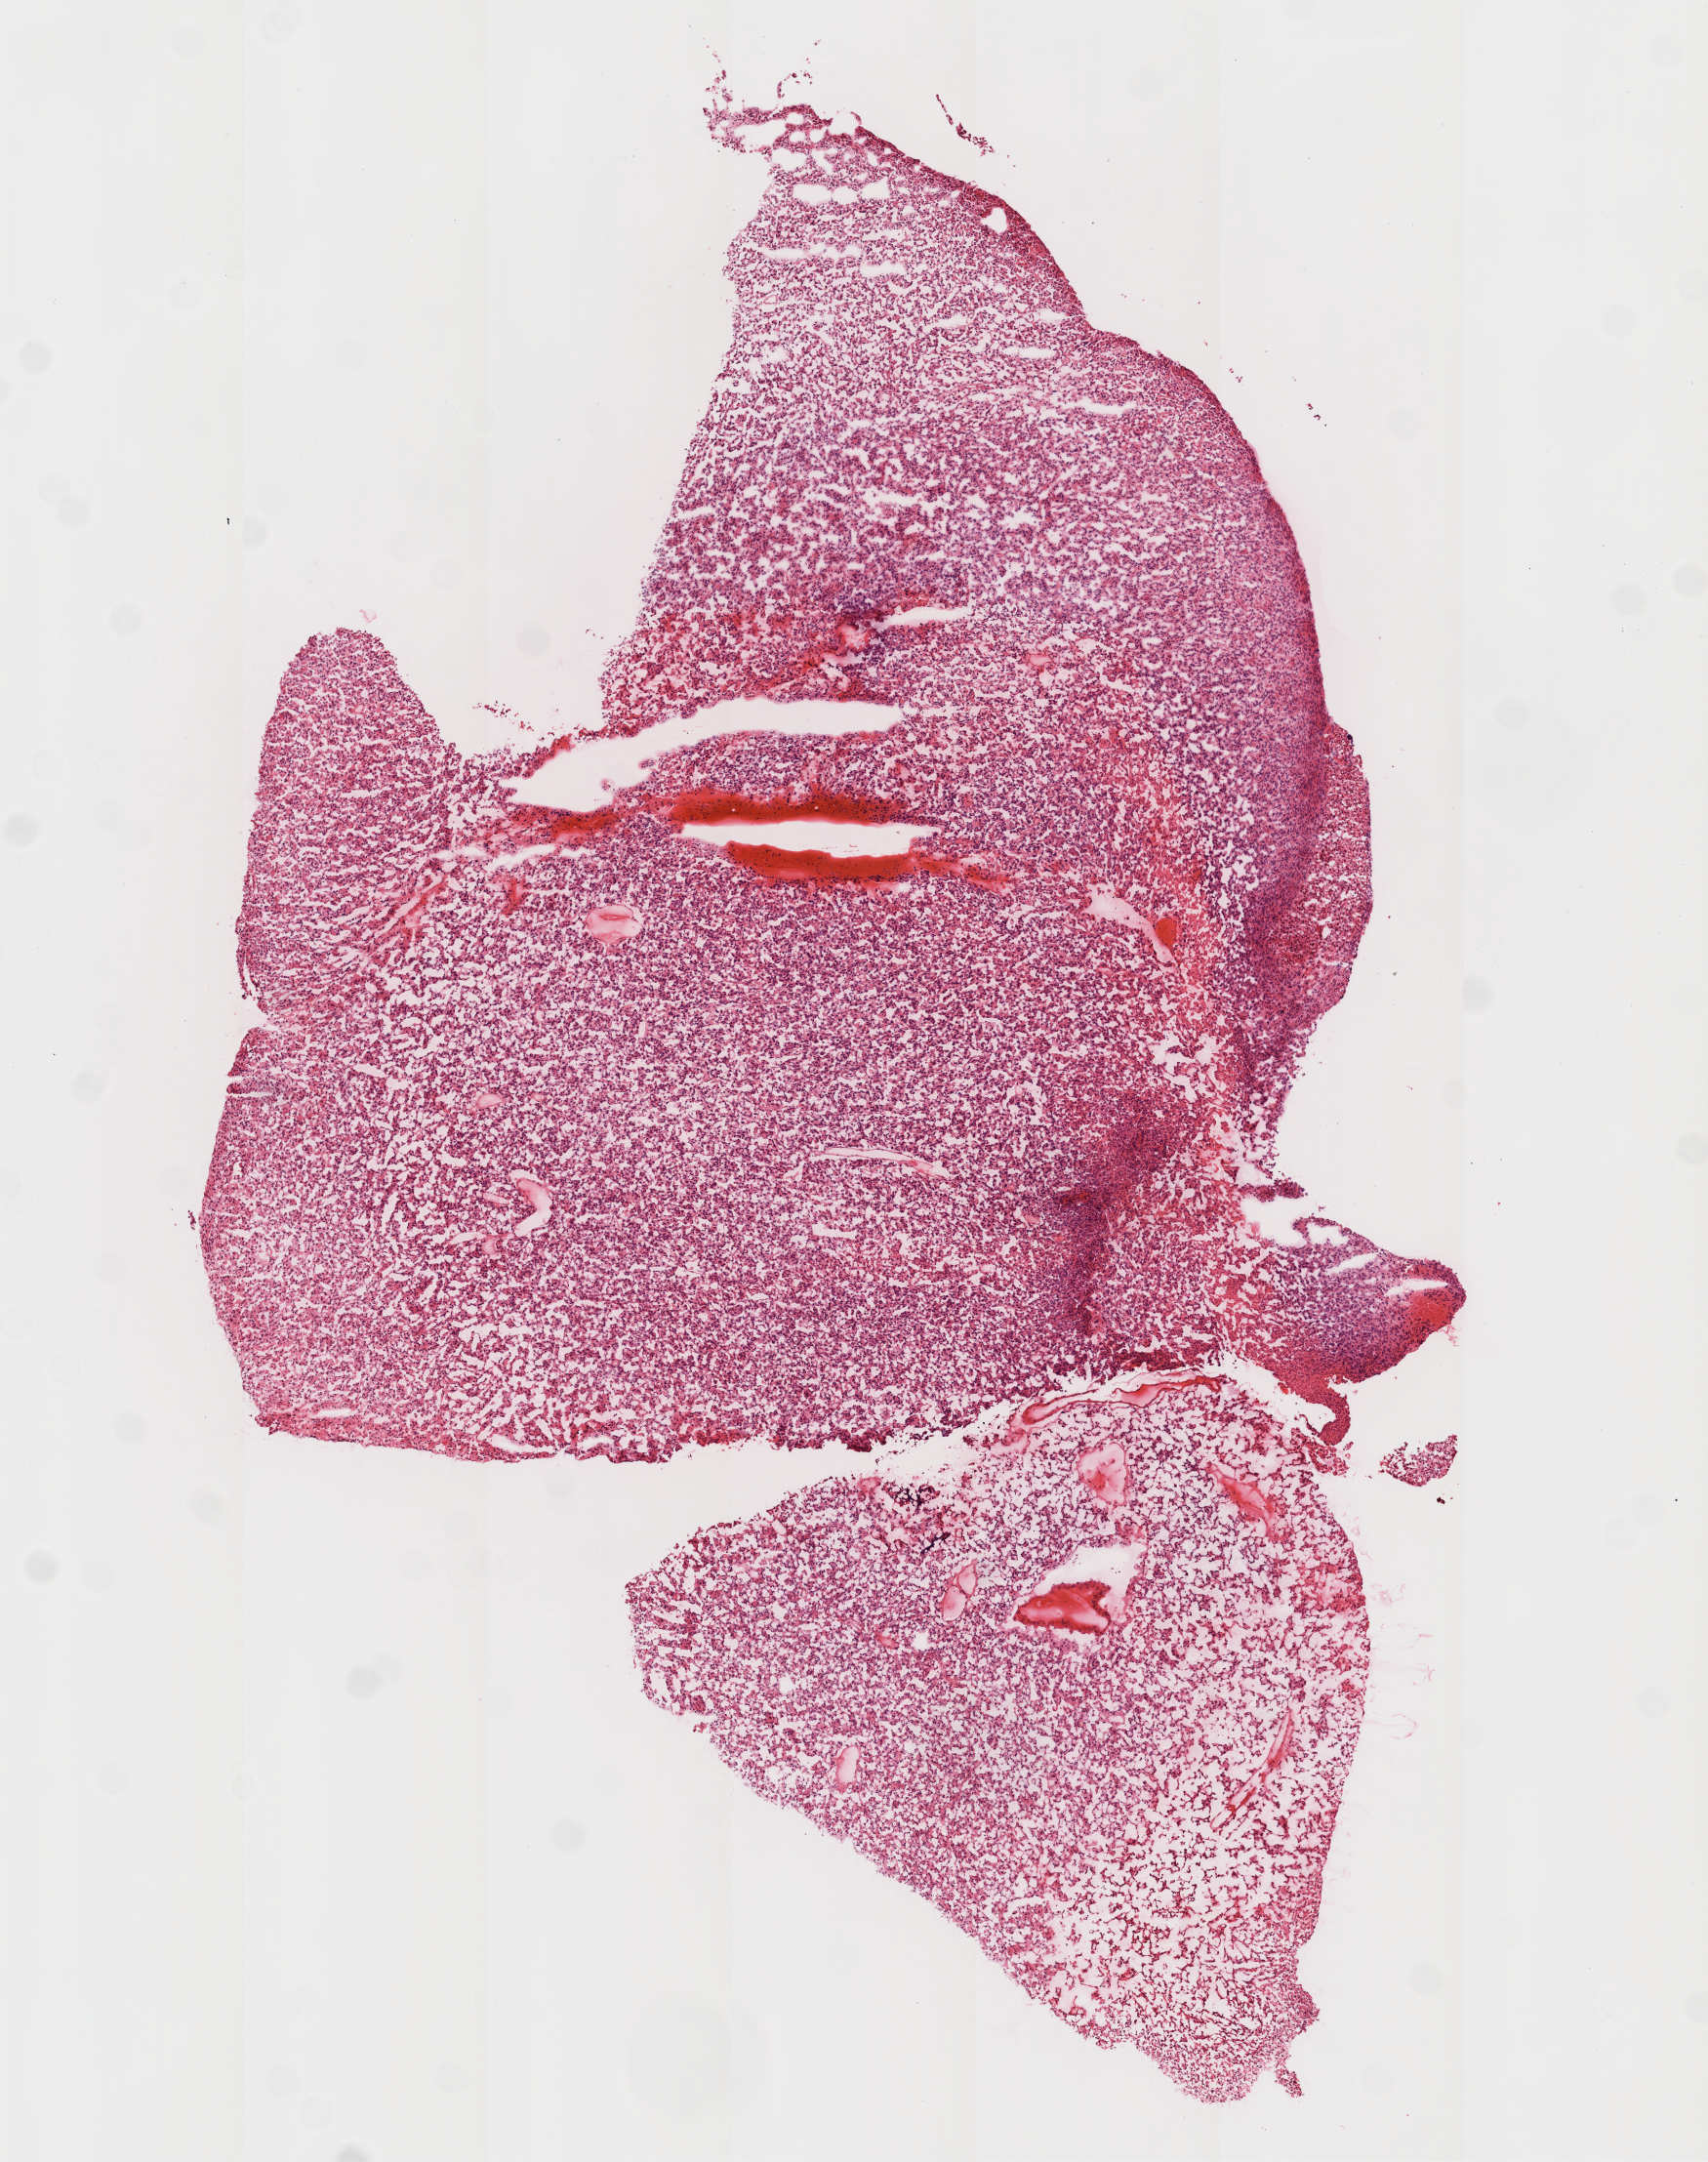
Whole-slide histology image, Hematoxylin and eosin (H&E) stained — shown as a low-resolution overview of the whole scanned area (about 7.0 x 8.9 mm), frozen section from the top of the tissue portion, brain, primary tumour sample. Patient: female, age at initial diagnosis 42 years. Histologic grade: G2 (moderately differentiated). Slide review estimates, as recorded: tumour cells 100%, tumour nuclei 80%, normal cells 0%, stromal cells 0%, necrosis 0%.
• pathologic diagnosis: Oligodendroglioma, NOS